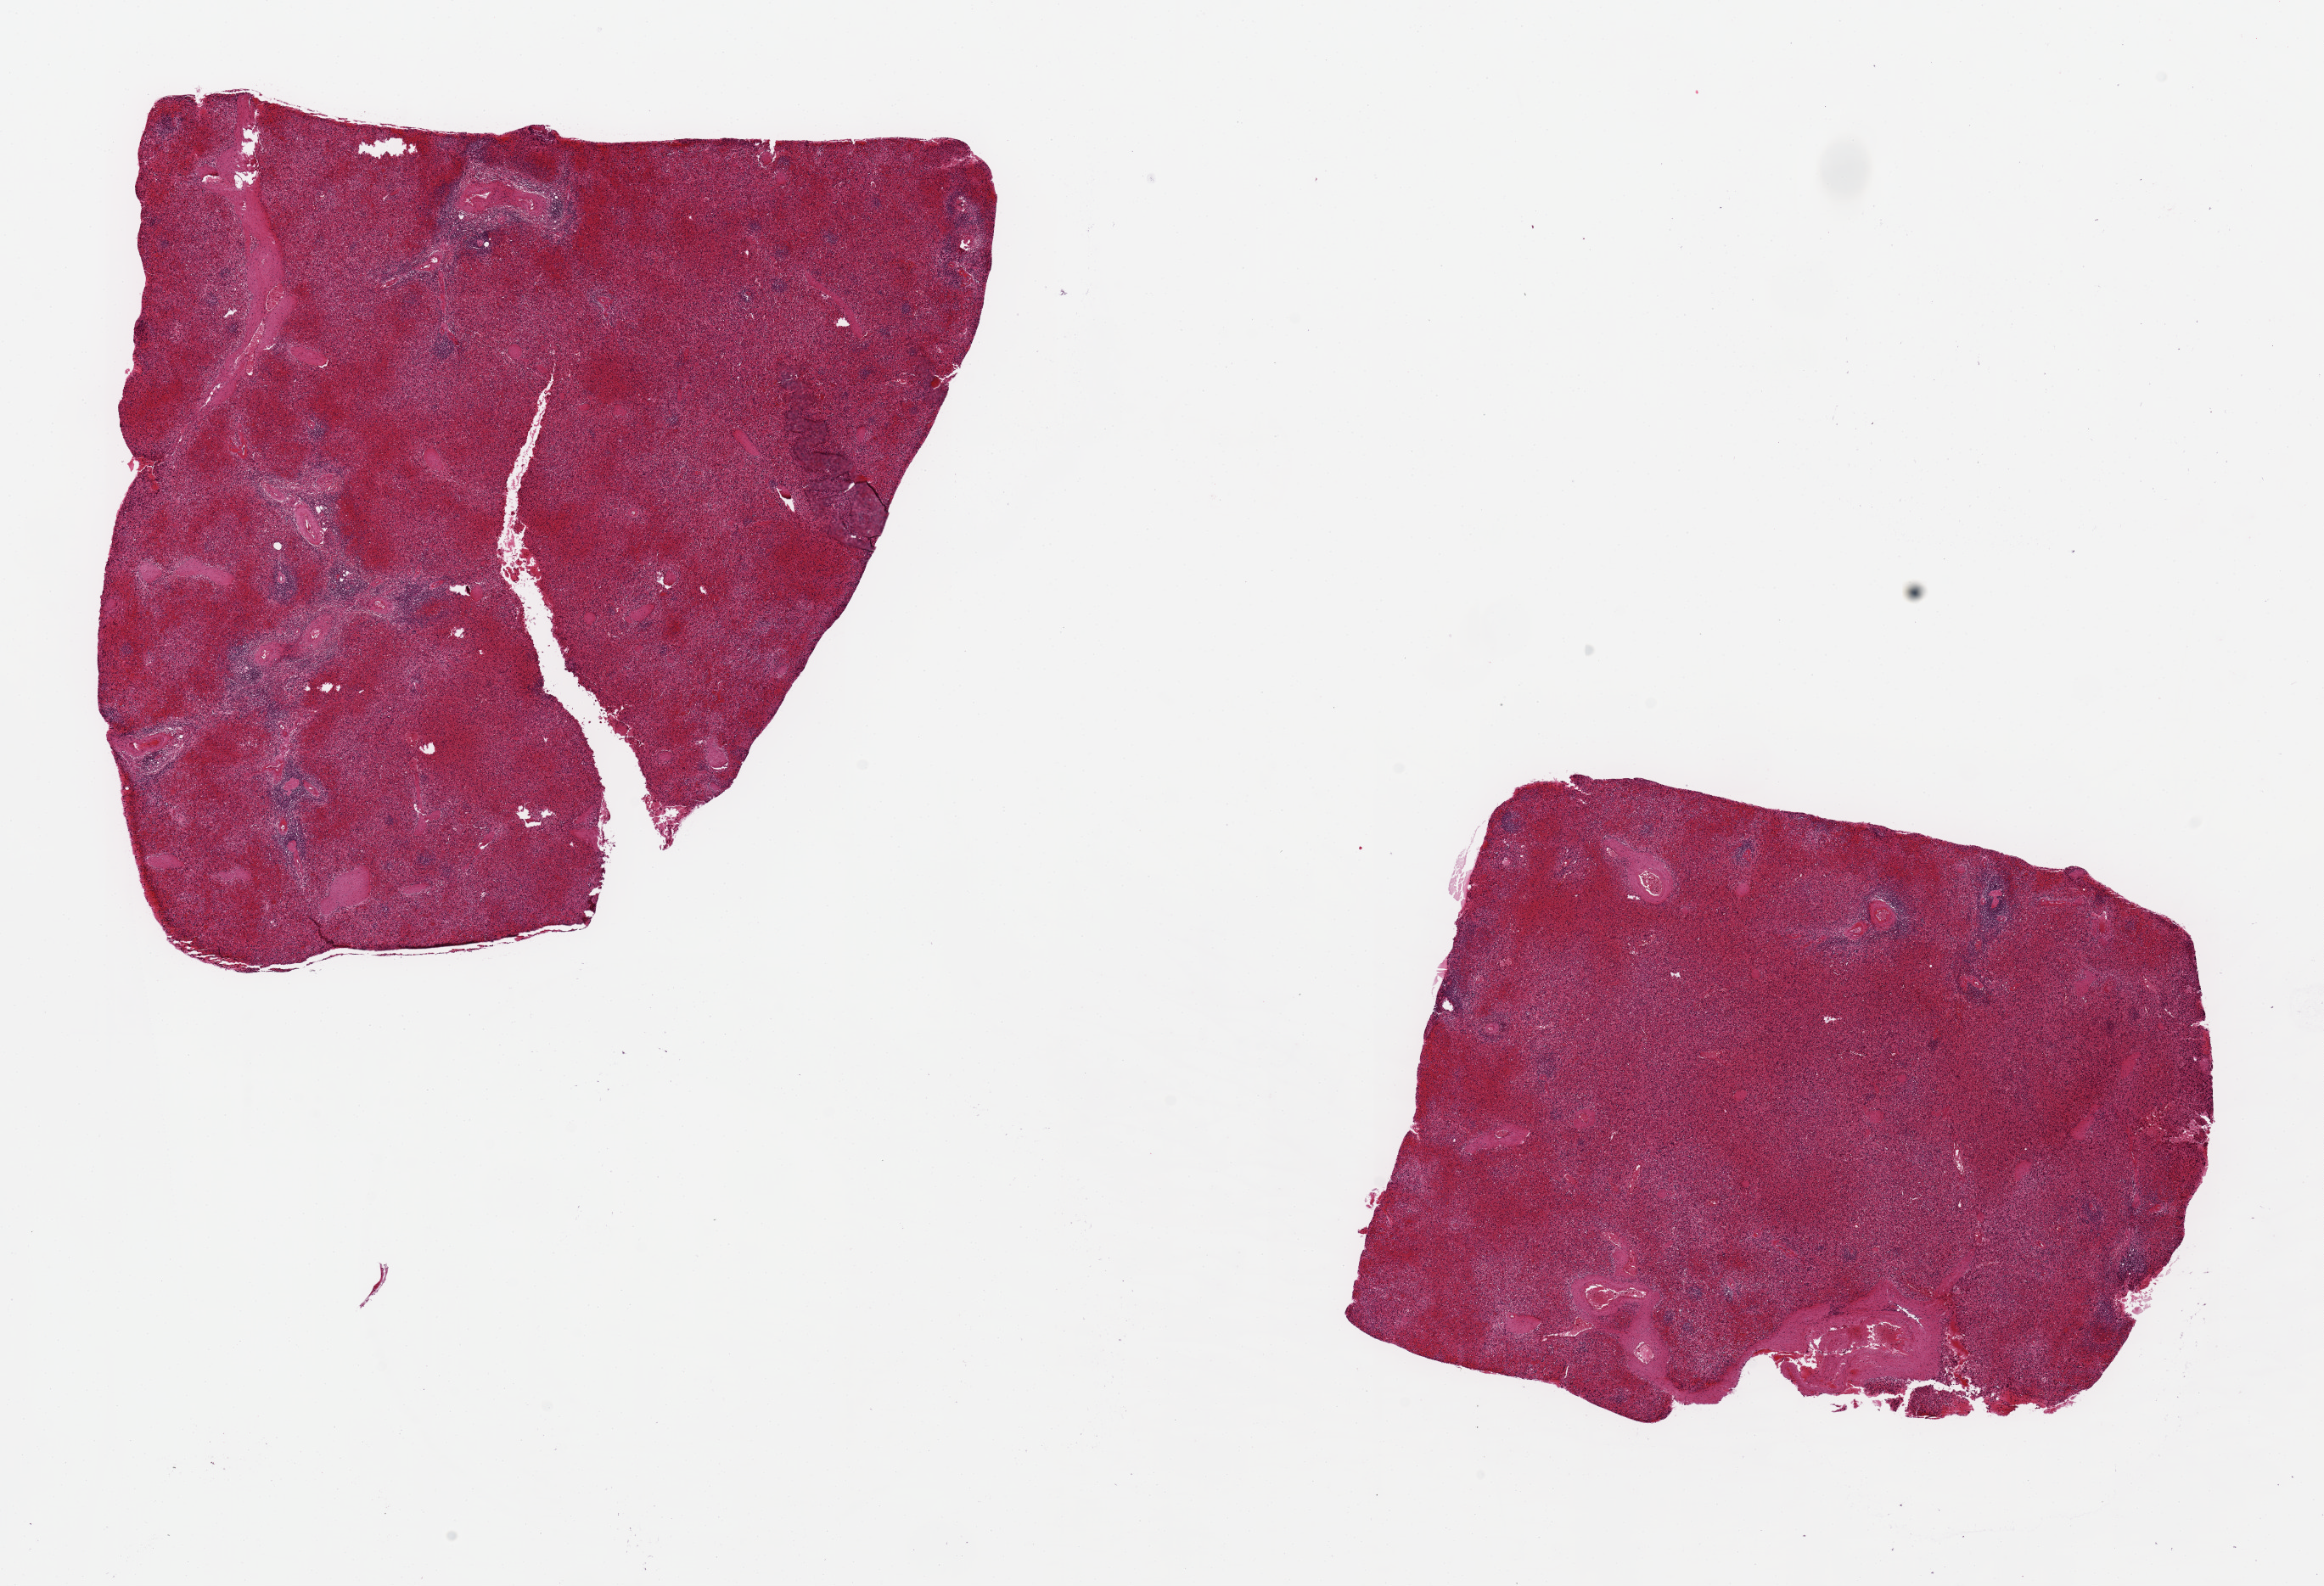
Whole-slide image, hematoxylin and eosin (H&E) stain, whole scanned area (about 21.7 x 14.8 mm) shown as a low-resolution overview, PAXgene-fixed paraffin-embedded (PFPE) section, section of spleen (target tissue), donor tissue sample.
Pathologist's review note for this sample: 2 pieces, ~ 7x6mm. Areas of poor/underfixation with tears/holes.